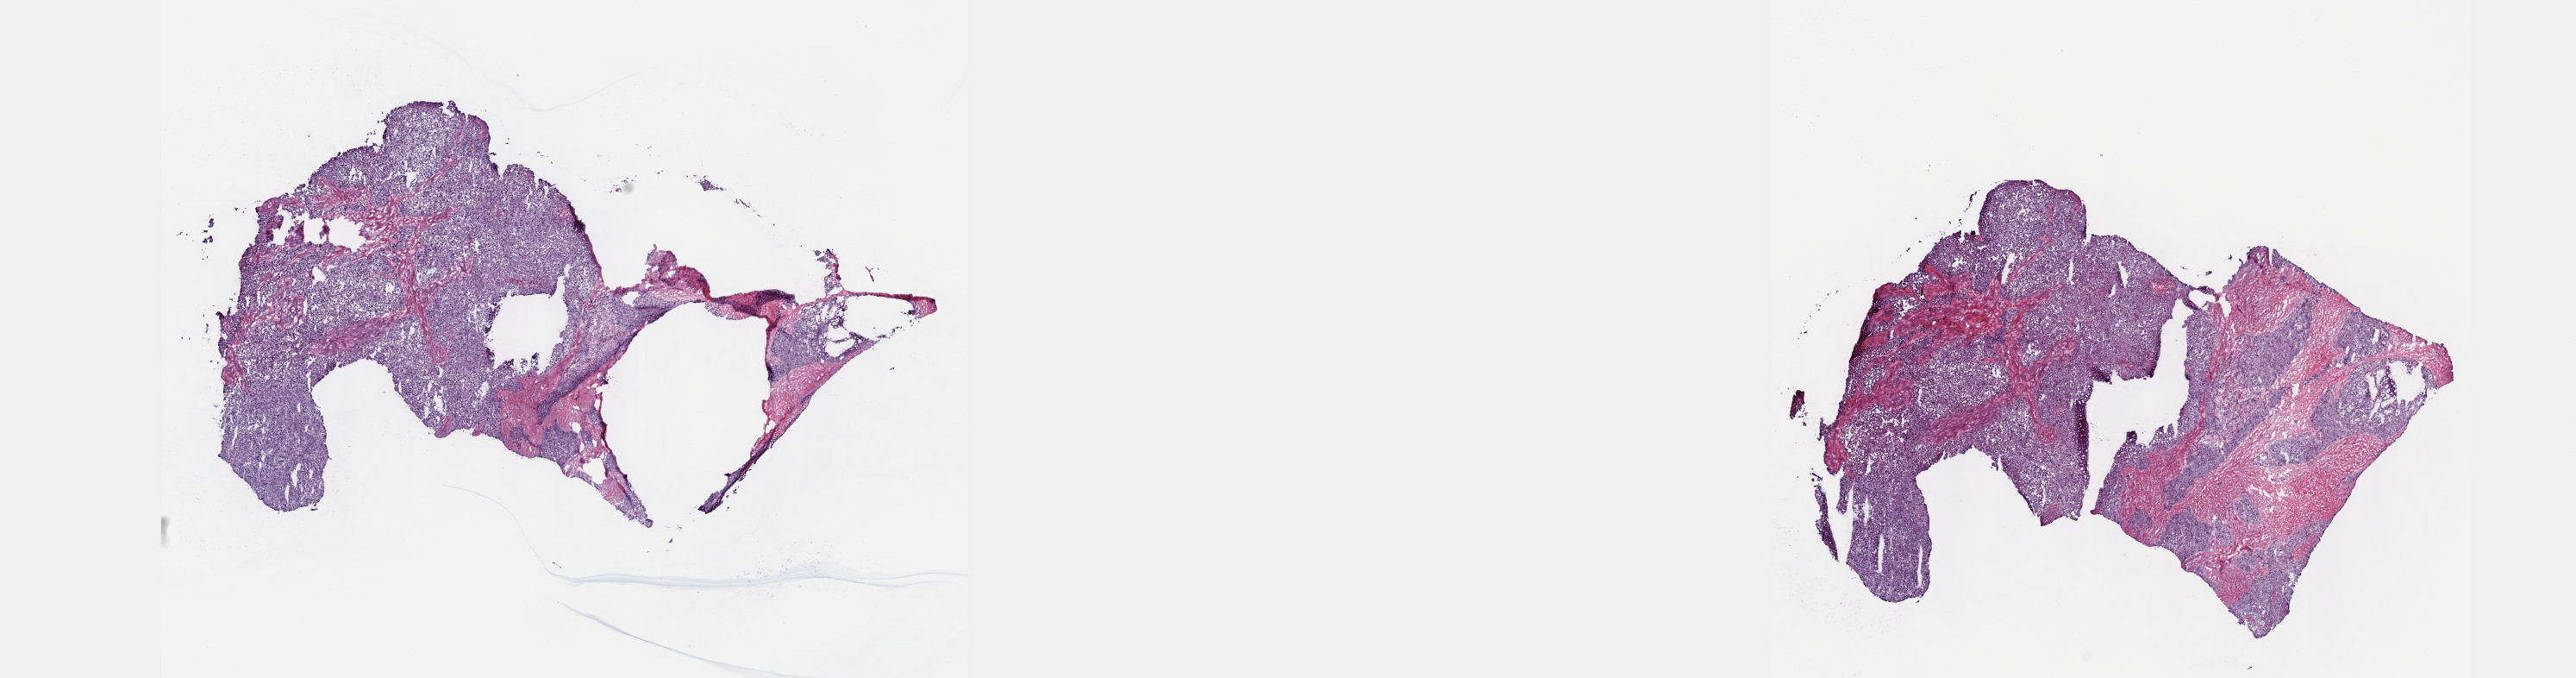
H&E-stained whole-slide image, low-resolution overview of the scanned area, about 24.1 x 6.4 mm (from a 40x scan). Frozen section from the top of the tissue portion. Sample: primary tumour, liver. Patient: female, age at initial diagnosis 56 years. Histologic grade: G2 (moderately differentiated). Composition of this section per pathologist review: tumour cells 75%, tumour nuclei 80%, normal cells 0%, stromal cells 25%, necrosis 0%. Inflammatory infiltration, as recorded: lymphocyte infiltration 0%, monocyte infiltration 0%, neutrophil infiltration 0%.
- histologic diagnosis: Hepatocellular carcinoma, NOS